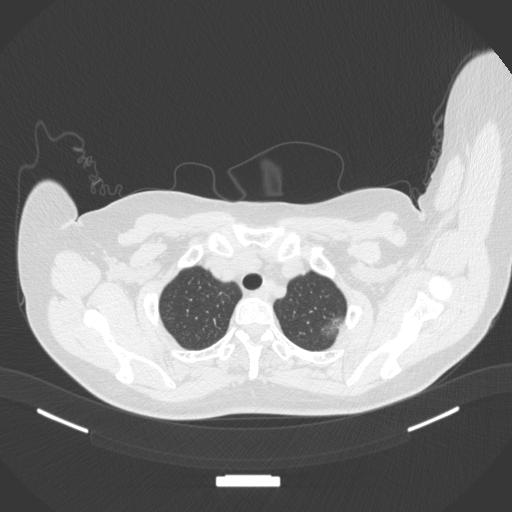
Chest CT, one axial slice; position 324 of 386 along the scan axis; reconstruction kernel B31f; lung window (W 1500 / L -600 HU); 1 mm slice thickness; 512 × 512 image matrix. Patient: female, 58 years. Case-level facts recorded for this patient, not image findings: clinical TNM (as recorded): T1c N0 M0.
Outlined on this slice (bounding box drawn by a radiologist):
- lung tumour (recorded histology: adenocarcinoma): bounding box [x1, y1, x2, y2] px = [319, 311, 345, 342]